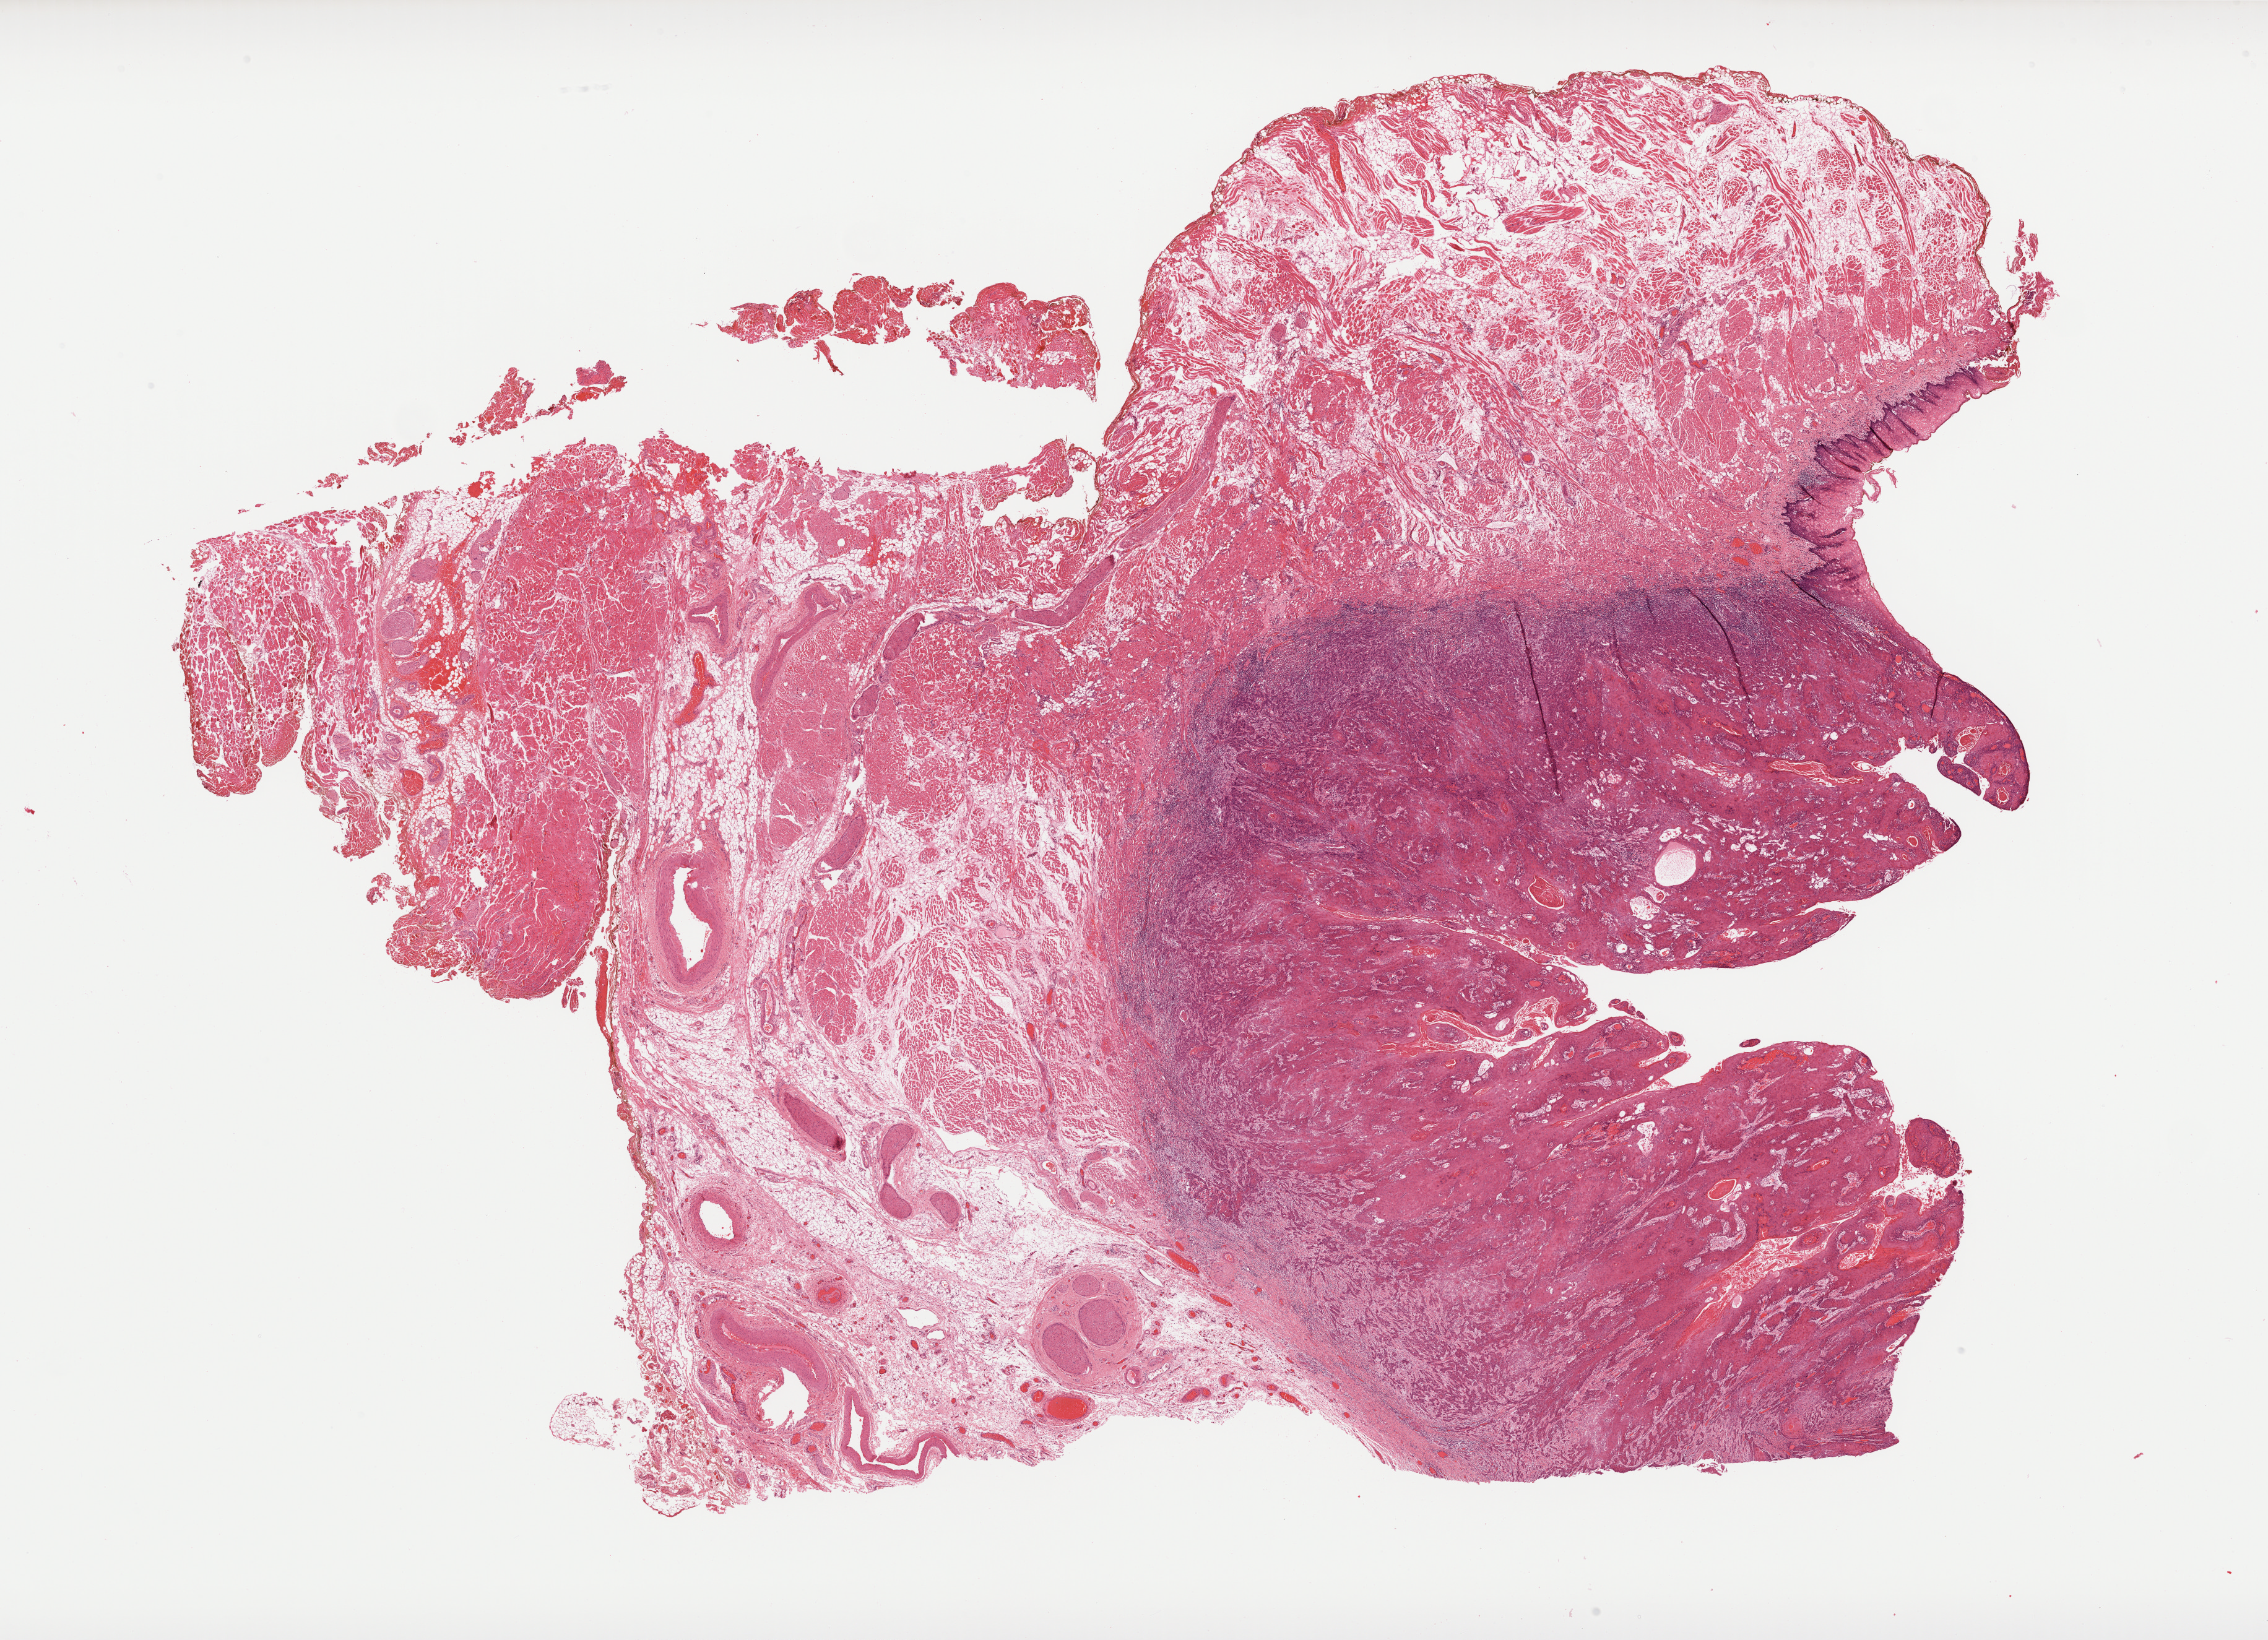
H&E-stained whole-slide image, shown as a low-resolution overview of the whole scanned area (about 29.5 x 21.3 mm, acquisition: 40x scan), formalin-fixed paraffin-embedded (FFPE) diagnostic section, primary tumour sample from the head and neck. Female, age 52 years at initial diagnosis.
Diagnosis: Squamous cell carcinoma, NOS (tongue, NOS).